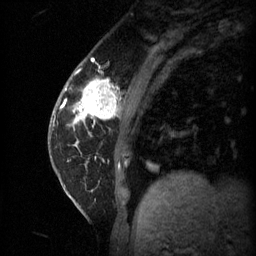
Breast MRI (dynamic contrast-enhanced), one sagittal slice; slice 15 of 60 in the series (ordered by position); 3 images stored at this slice position (order not interpretable as contrast timing); 1.5 T; TE 4.2 ms, TR 11 ms; 2 mm slice thickness; 256 × 256 image matrix, field of view 180 × 180 mm. Female patient, age 62 years.
Outlined on this slice (semi-automatic segmentation, software-assisted and operator-edited):
- analysis volume of interest (the breast-tissue region the enhancement analysis was run in; not a lesion): bounding box (x1, y1, x2, y2) in pixels: (55, 72, 124, 135)
- tumour enhancement mask (voxels above the 70 % enhancement threshold inside the analysis volume of interest): (64, 80, 119, 125)